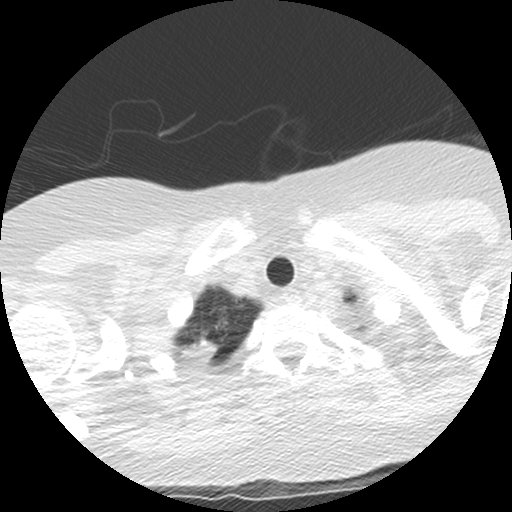
Low-dose screening chest CT, one axial slice; slice 122 of 130 in the series (ordered by position); reconstruction kernel STANDARD; lung window (W 1500 / L -600 HU); 2.5 mm slice thickness; 512 × 512 image matrix, field of view 290 × 290 mm.
Outlined on this slice (manually delineated by an expert):
- lesion 1 (tumor, upper lobe of right lung): bounding box <189,340,216,362> (left, top, right, bottom; pixels)